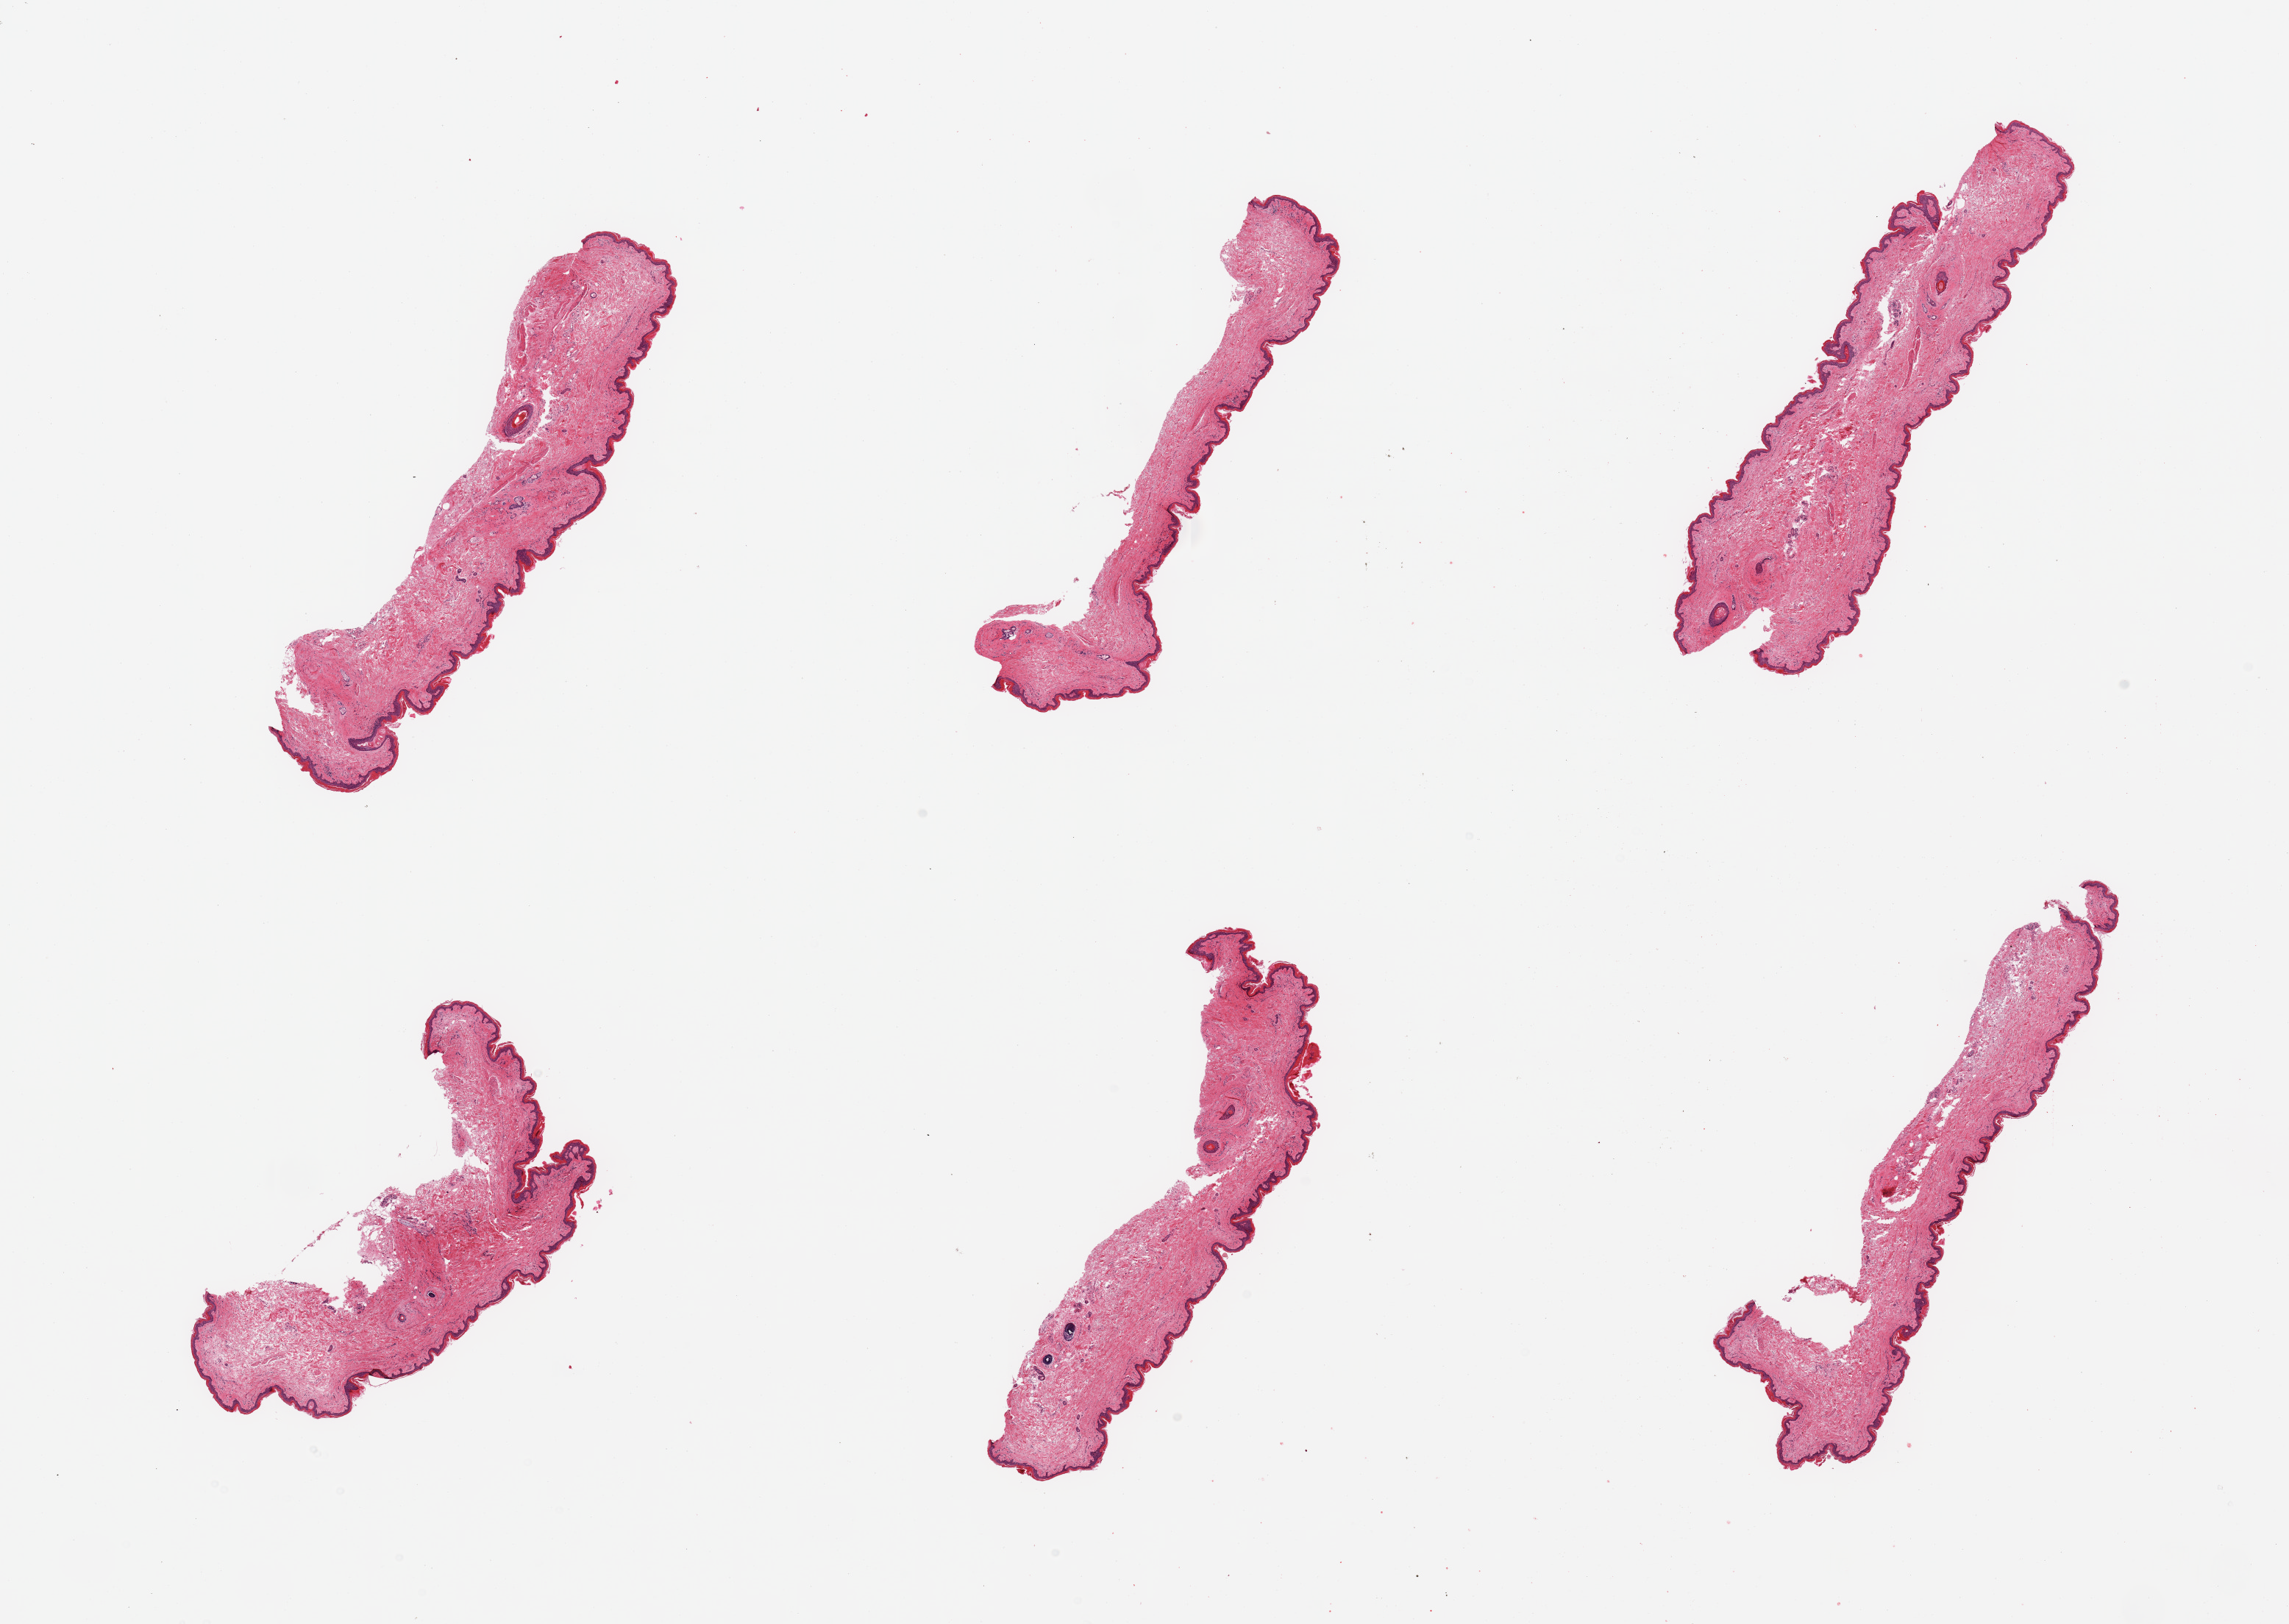
Hematoxylin and eosin (H&E) whole-slide image, shown as a low-resolution overview of the whole scanned area (about 24.6 x 17.5 mm). PAXgene-fixed paraffin-embedded (PFPE) section. Target tissue: skin of suprapubic region. Tissue donor sample. Donor sex: female.
Reviewer comment on this tissue sample: 6 pieces, squamous epithelium up to !30-40 microns. Minimal dermal fat.